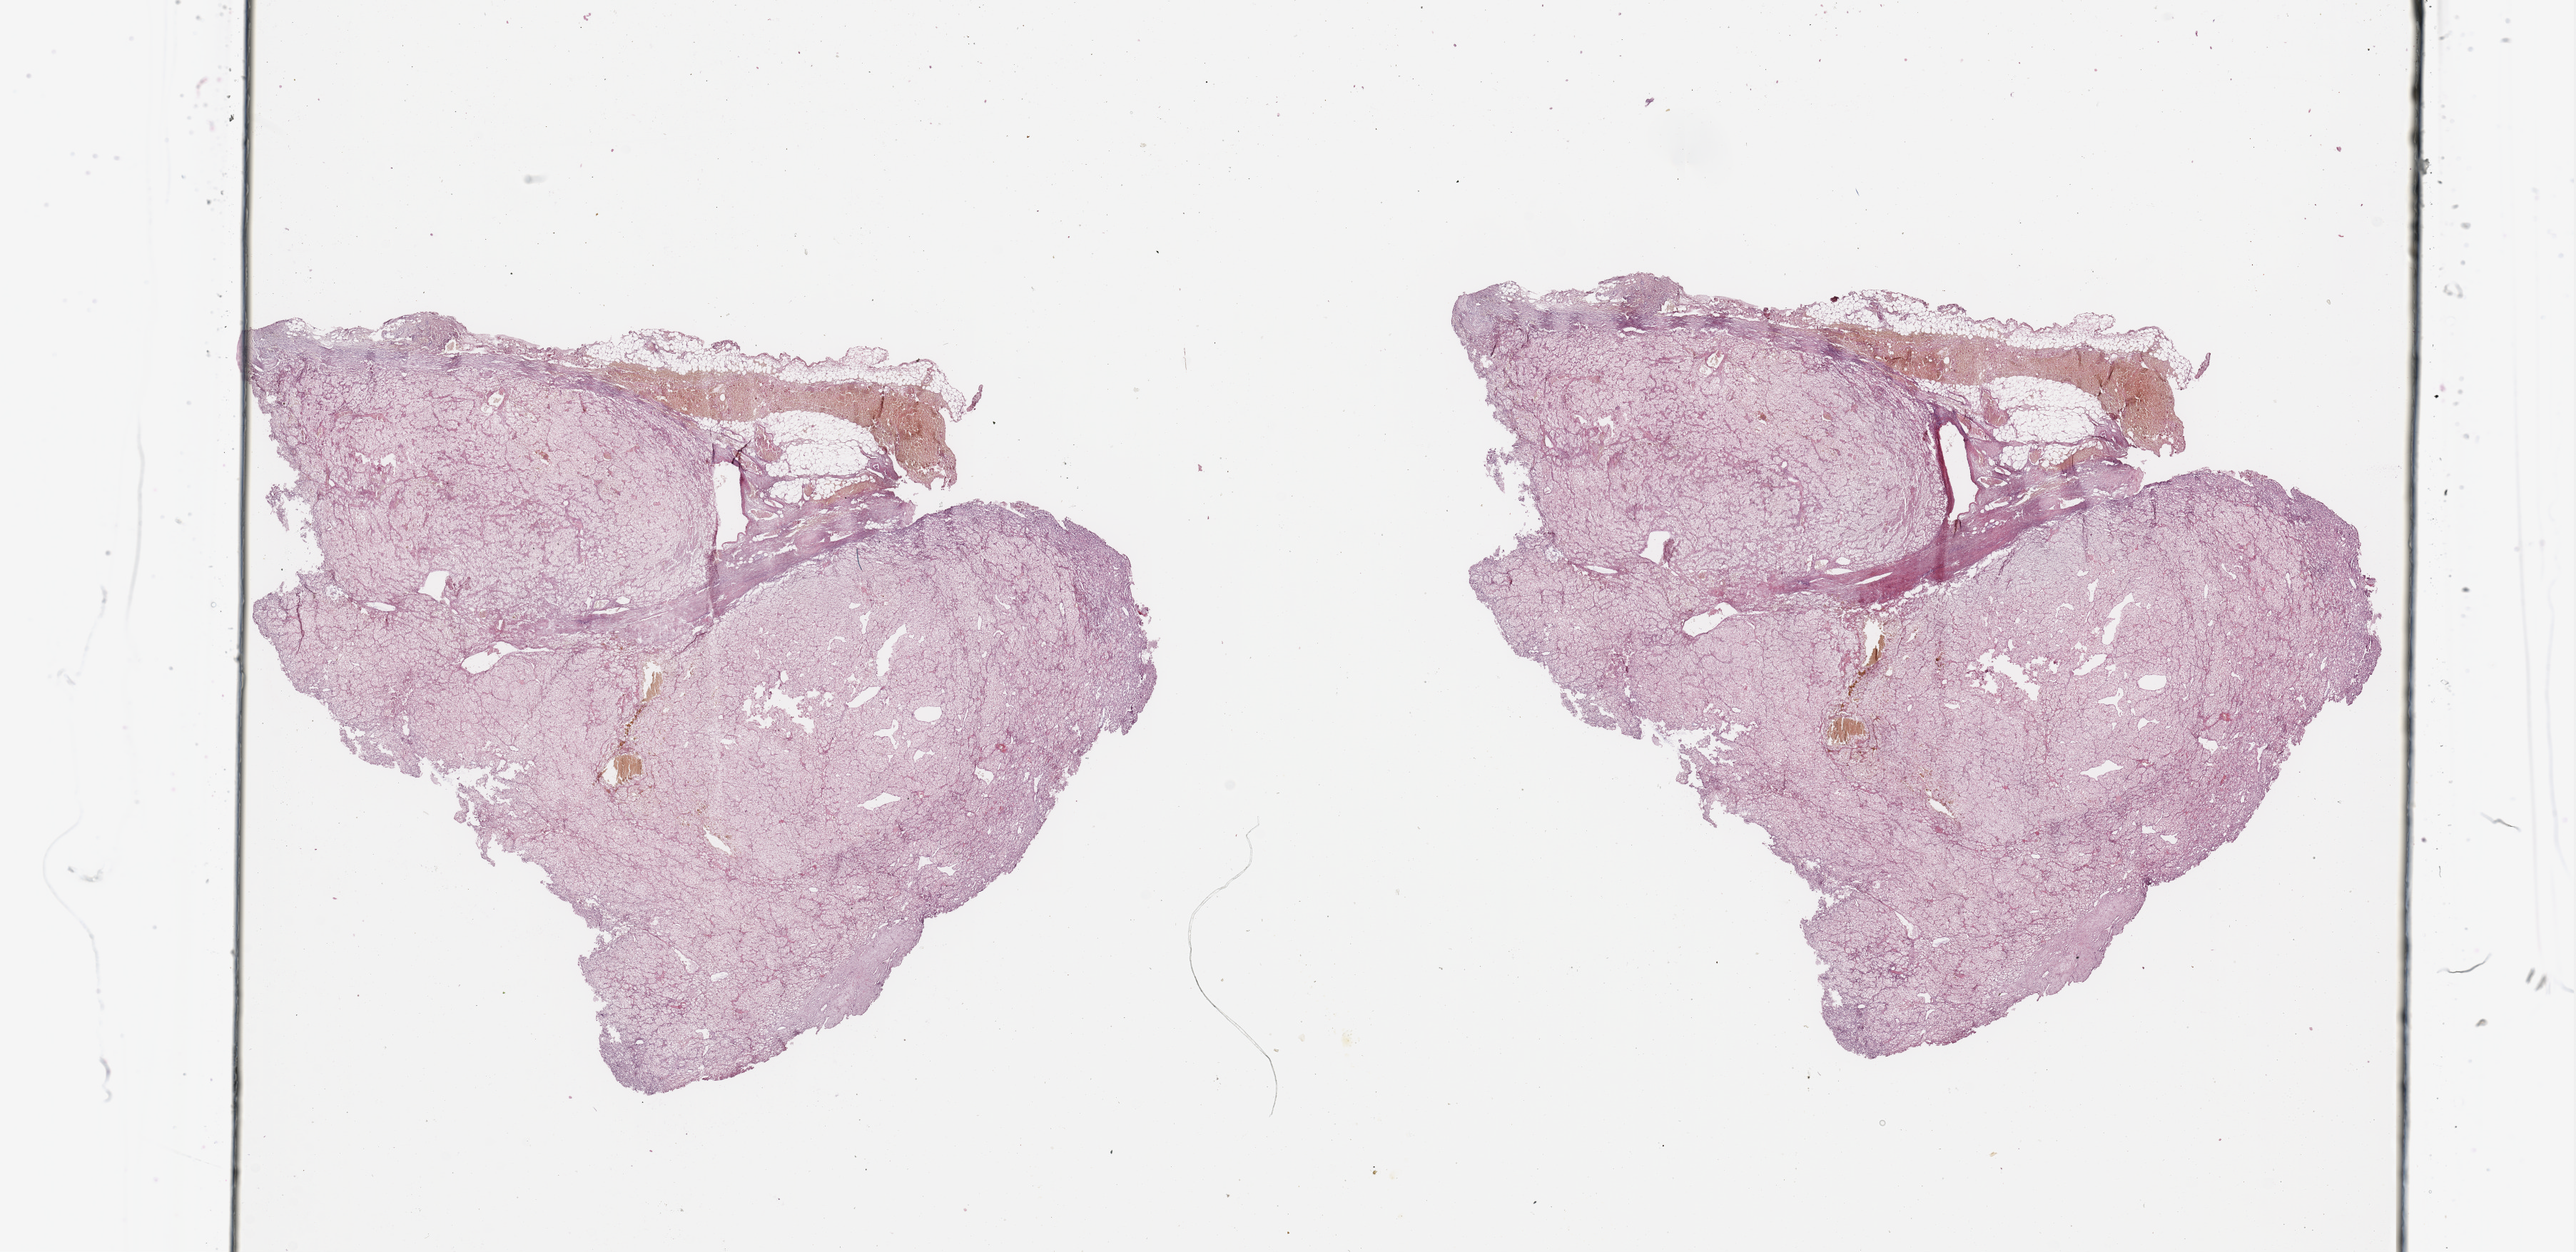
H&E-stained whole-slide image — a low-resolution overview of the entire scanned area, about 28.5 x 13.9 mm (slide scanned at 20x); kidney, tumour tissue. Female, 86 y/o. Histologic grade: G3 (poorly differentiated).
- histologic diagnosis: Renal cell carcinoma, NOS
- primary tumour site (as recorded): upper pole
- AJCC pathologic stage: IV